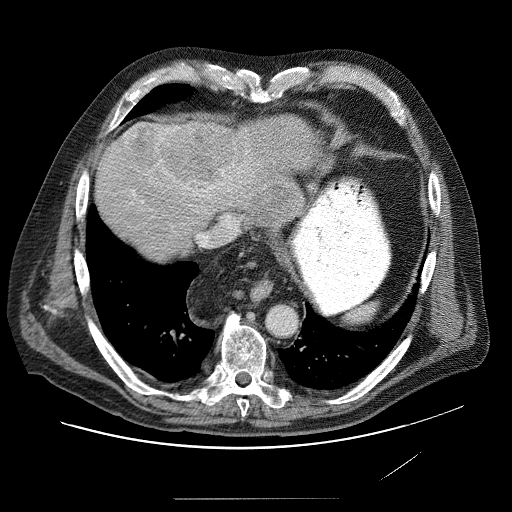
Contrast-enhanced abdominal CT (liver protocol), one axial slice. Slice 72 of 89 in the series (ordered by position). Reconstruction kernel STANDARD. Soft-tissue window (W 400 / L 40 HU). 2.5 mm slice thickness. 512 × 512 image matrix, field of view 420 × 420 mm. From the clinical record (not read from this slice): diagnosis: hepatocellular carcinoma (patient treated with transarterial chemoembolisation; whether this scan precedes or follows treatment is not stated here); TNM stage (as recorded): Stage-IVA; Child-Pugh class: A.
Structures marked on this image (semi-automatic segmentation, software-assisted and operator-edited):
- liver parenchyma outside the tumour (the mass and vessels are separate outlines, so this box may not span the whole liver): bounding box [x1, y1, x2, y2] px = [98, 118, 301, 244]
- mass: [123, 116, 298, 219]
- liver vessels: [128, 158, 247, 244]